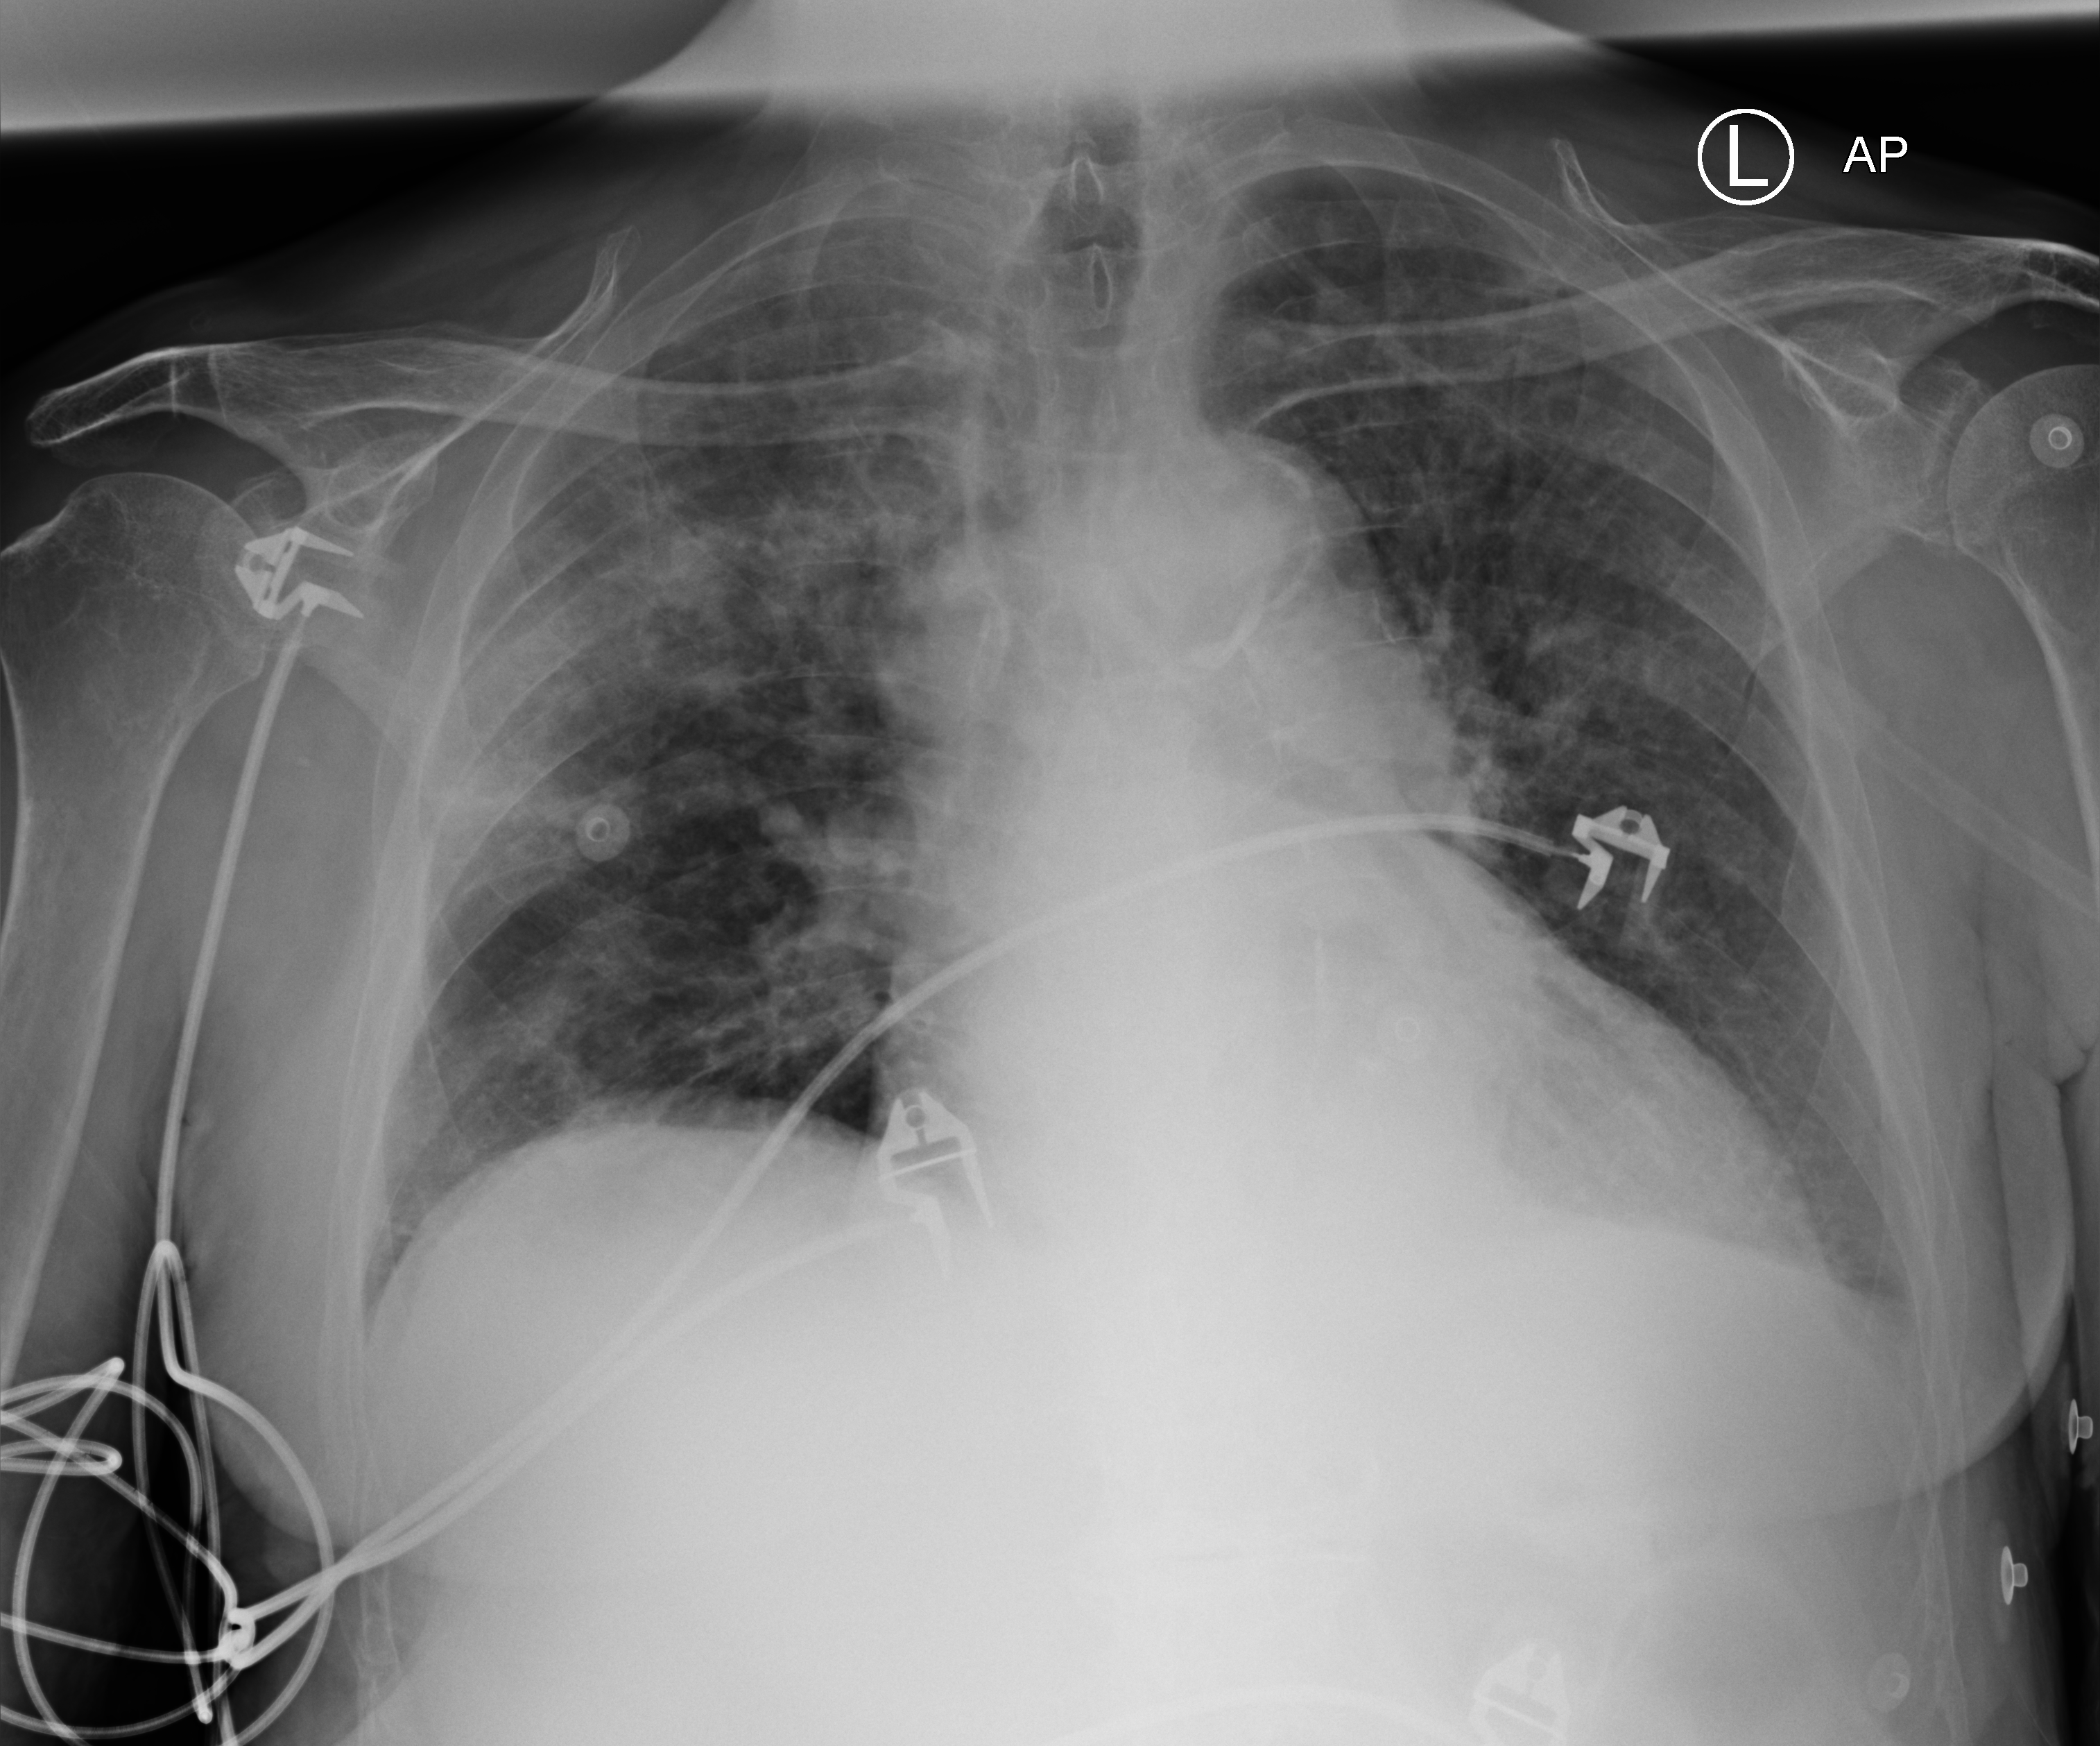
Chest X-ray (portable); anteroposterior (AP) projection. Patient hospitalised with COVID-19; male, aged 75–90 years.
Admission-level facts for this patient (not findings on this image; timing relative to this image not recorded): mechanically ventilated during this hospital stay: no.